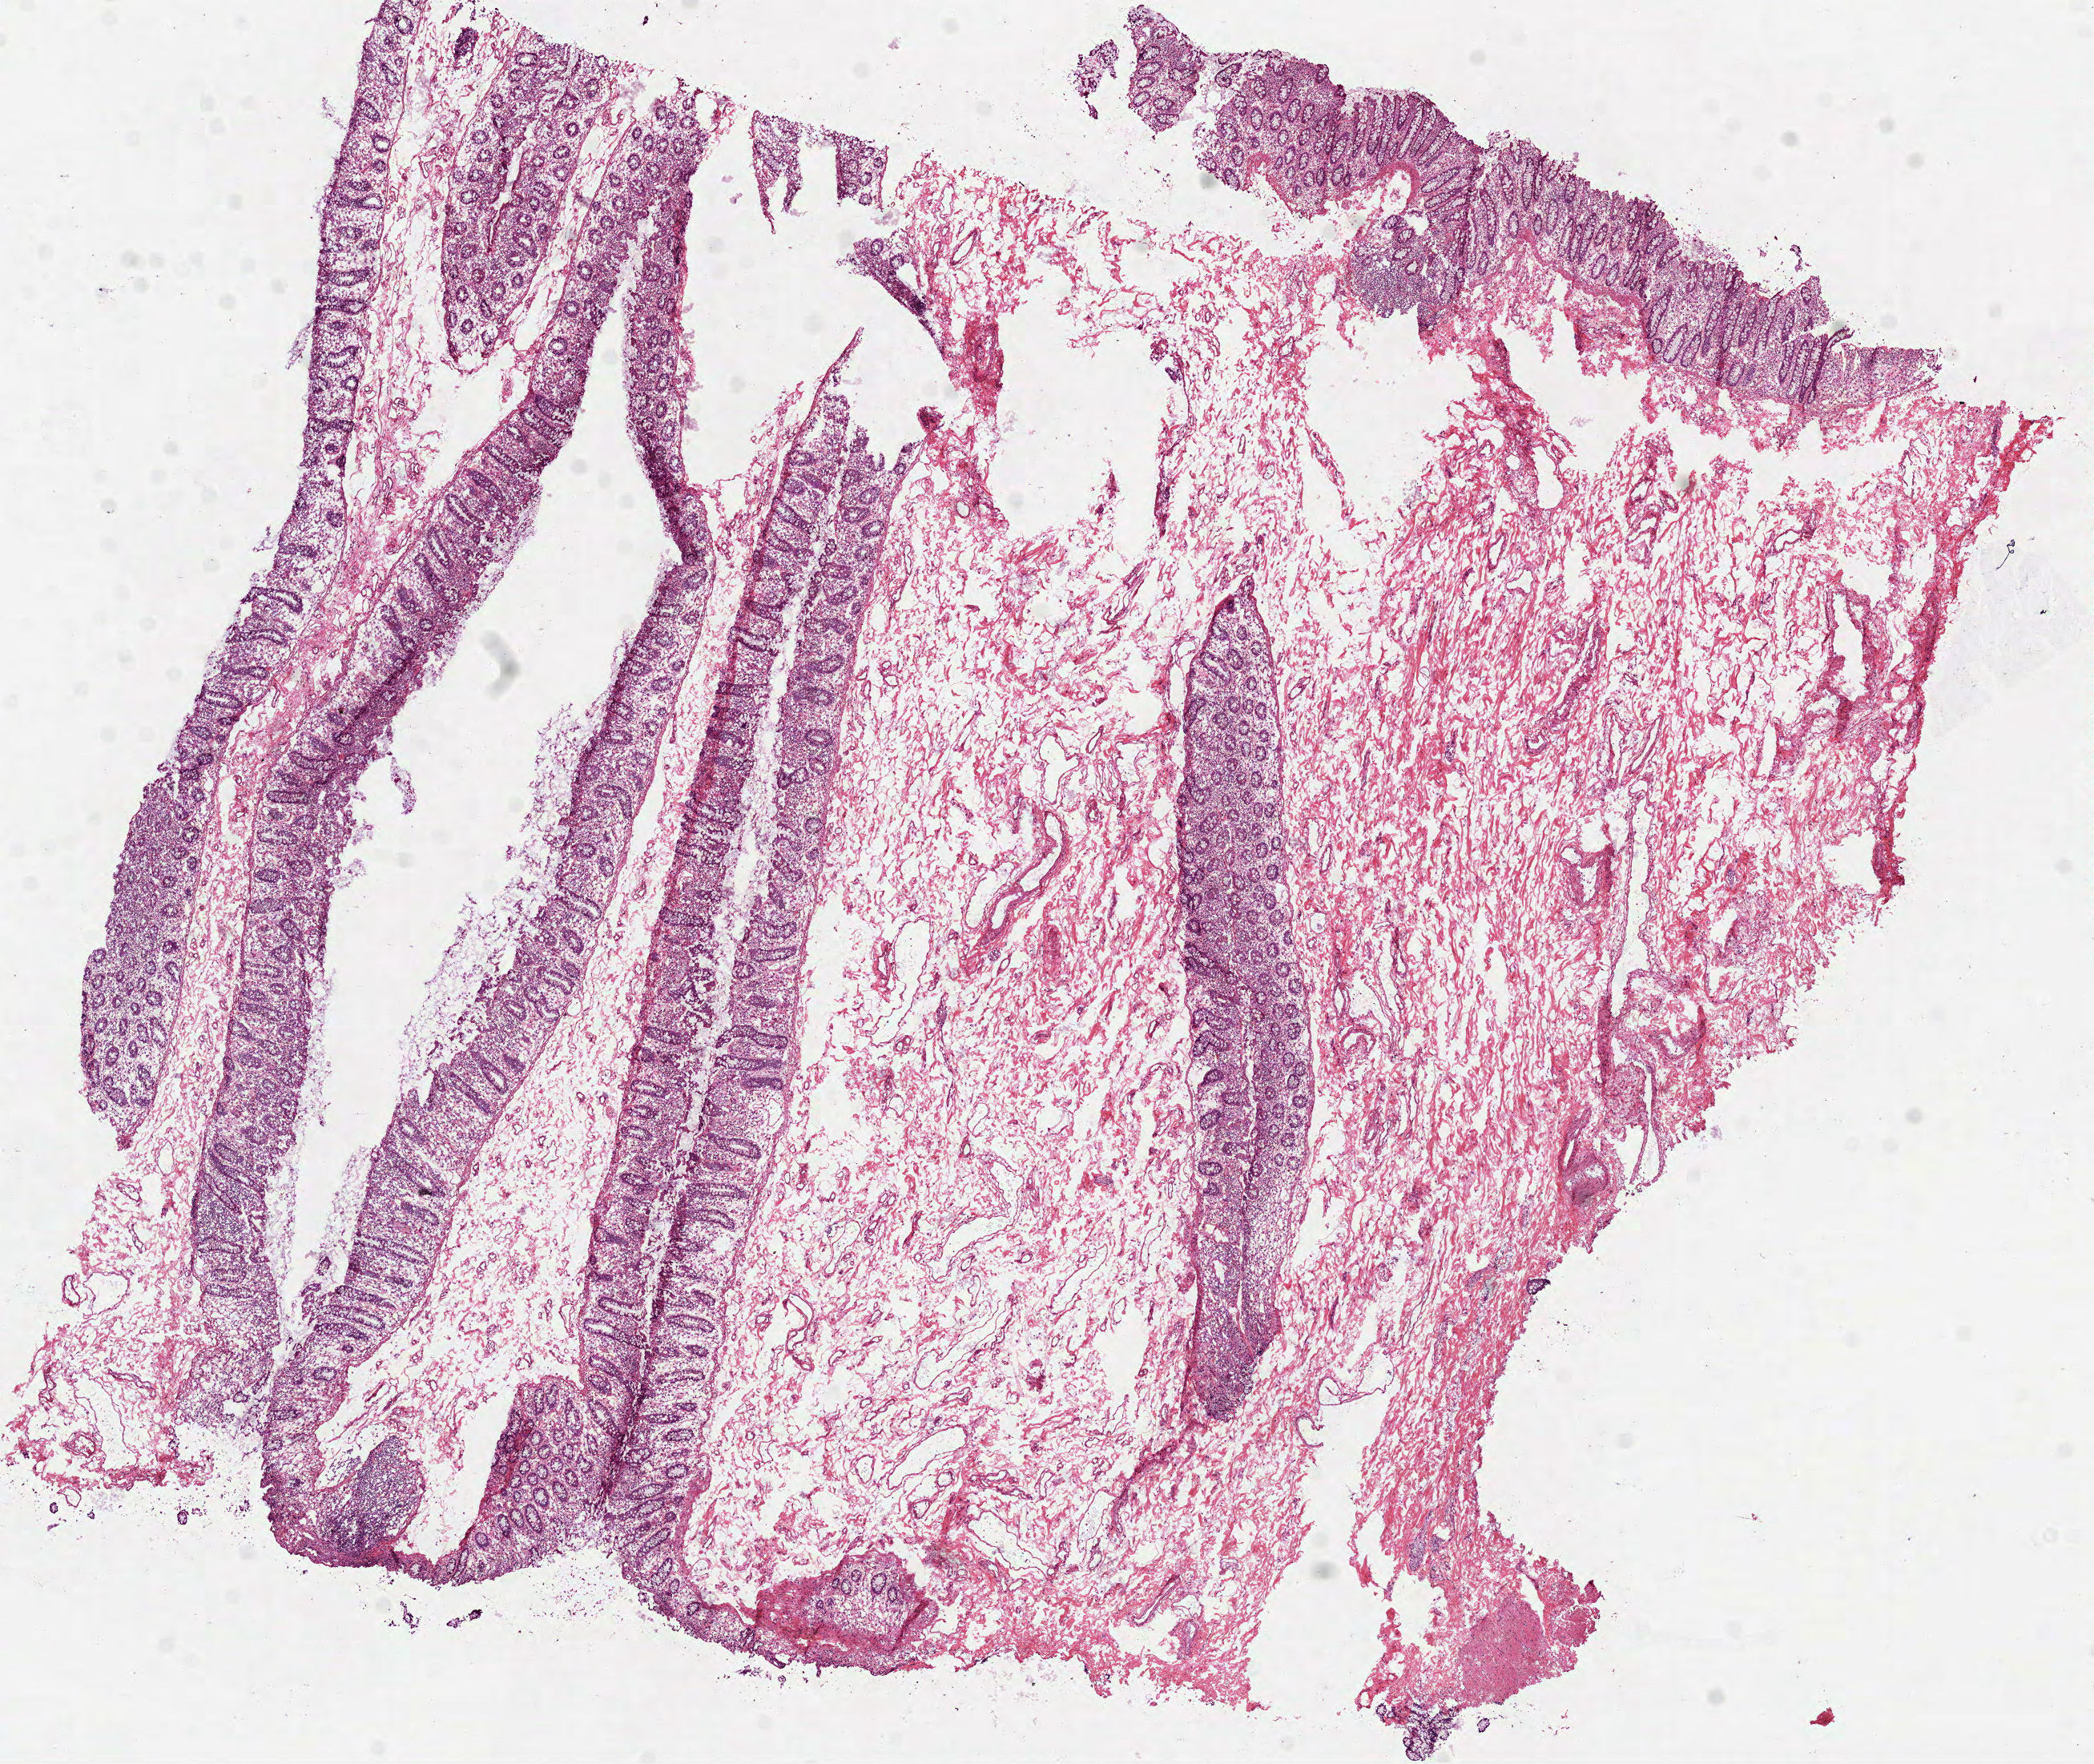
H&E whole-slide image, a low-resolution overview of the entire scanned area, about 10.5 x 8.9 mm (from a 40x scan), frozen section from the top of the tissue portion, sample: solid tissue normal (non-tumour tissue), colon. Patient: male, age at initial diagnosis 64 years.
- this section: solid tissue normal (non-tumour) sample from the same patient
- patient diagnosis: Adenocarcinoma, NOS (ascending colon)